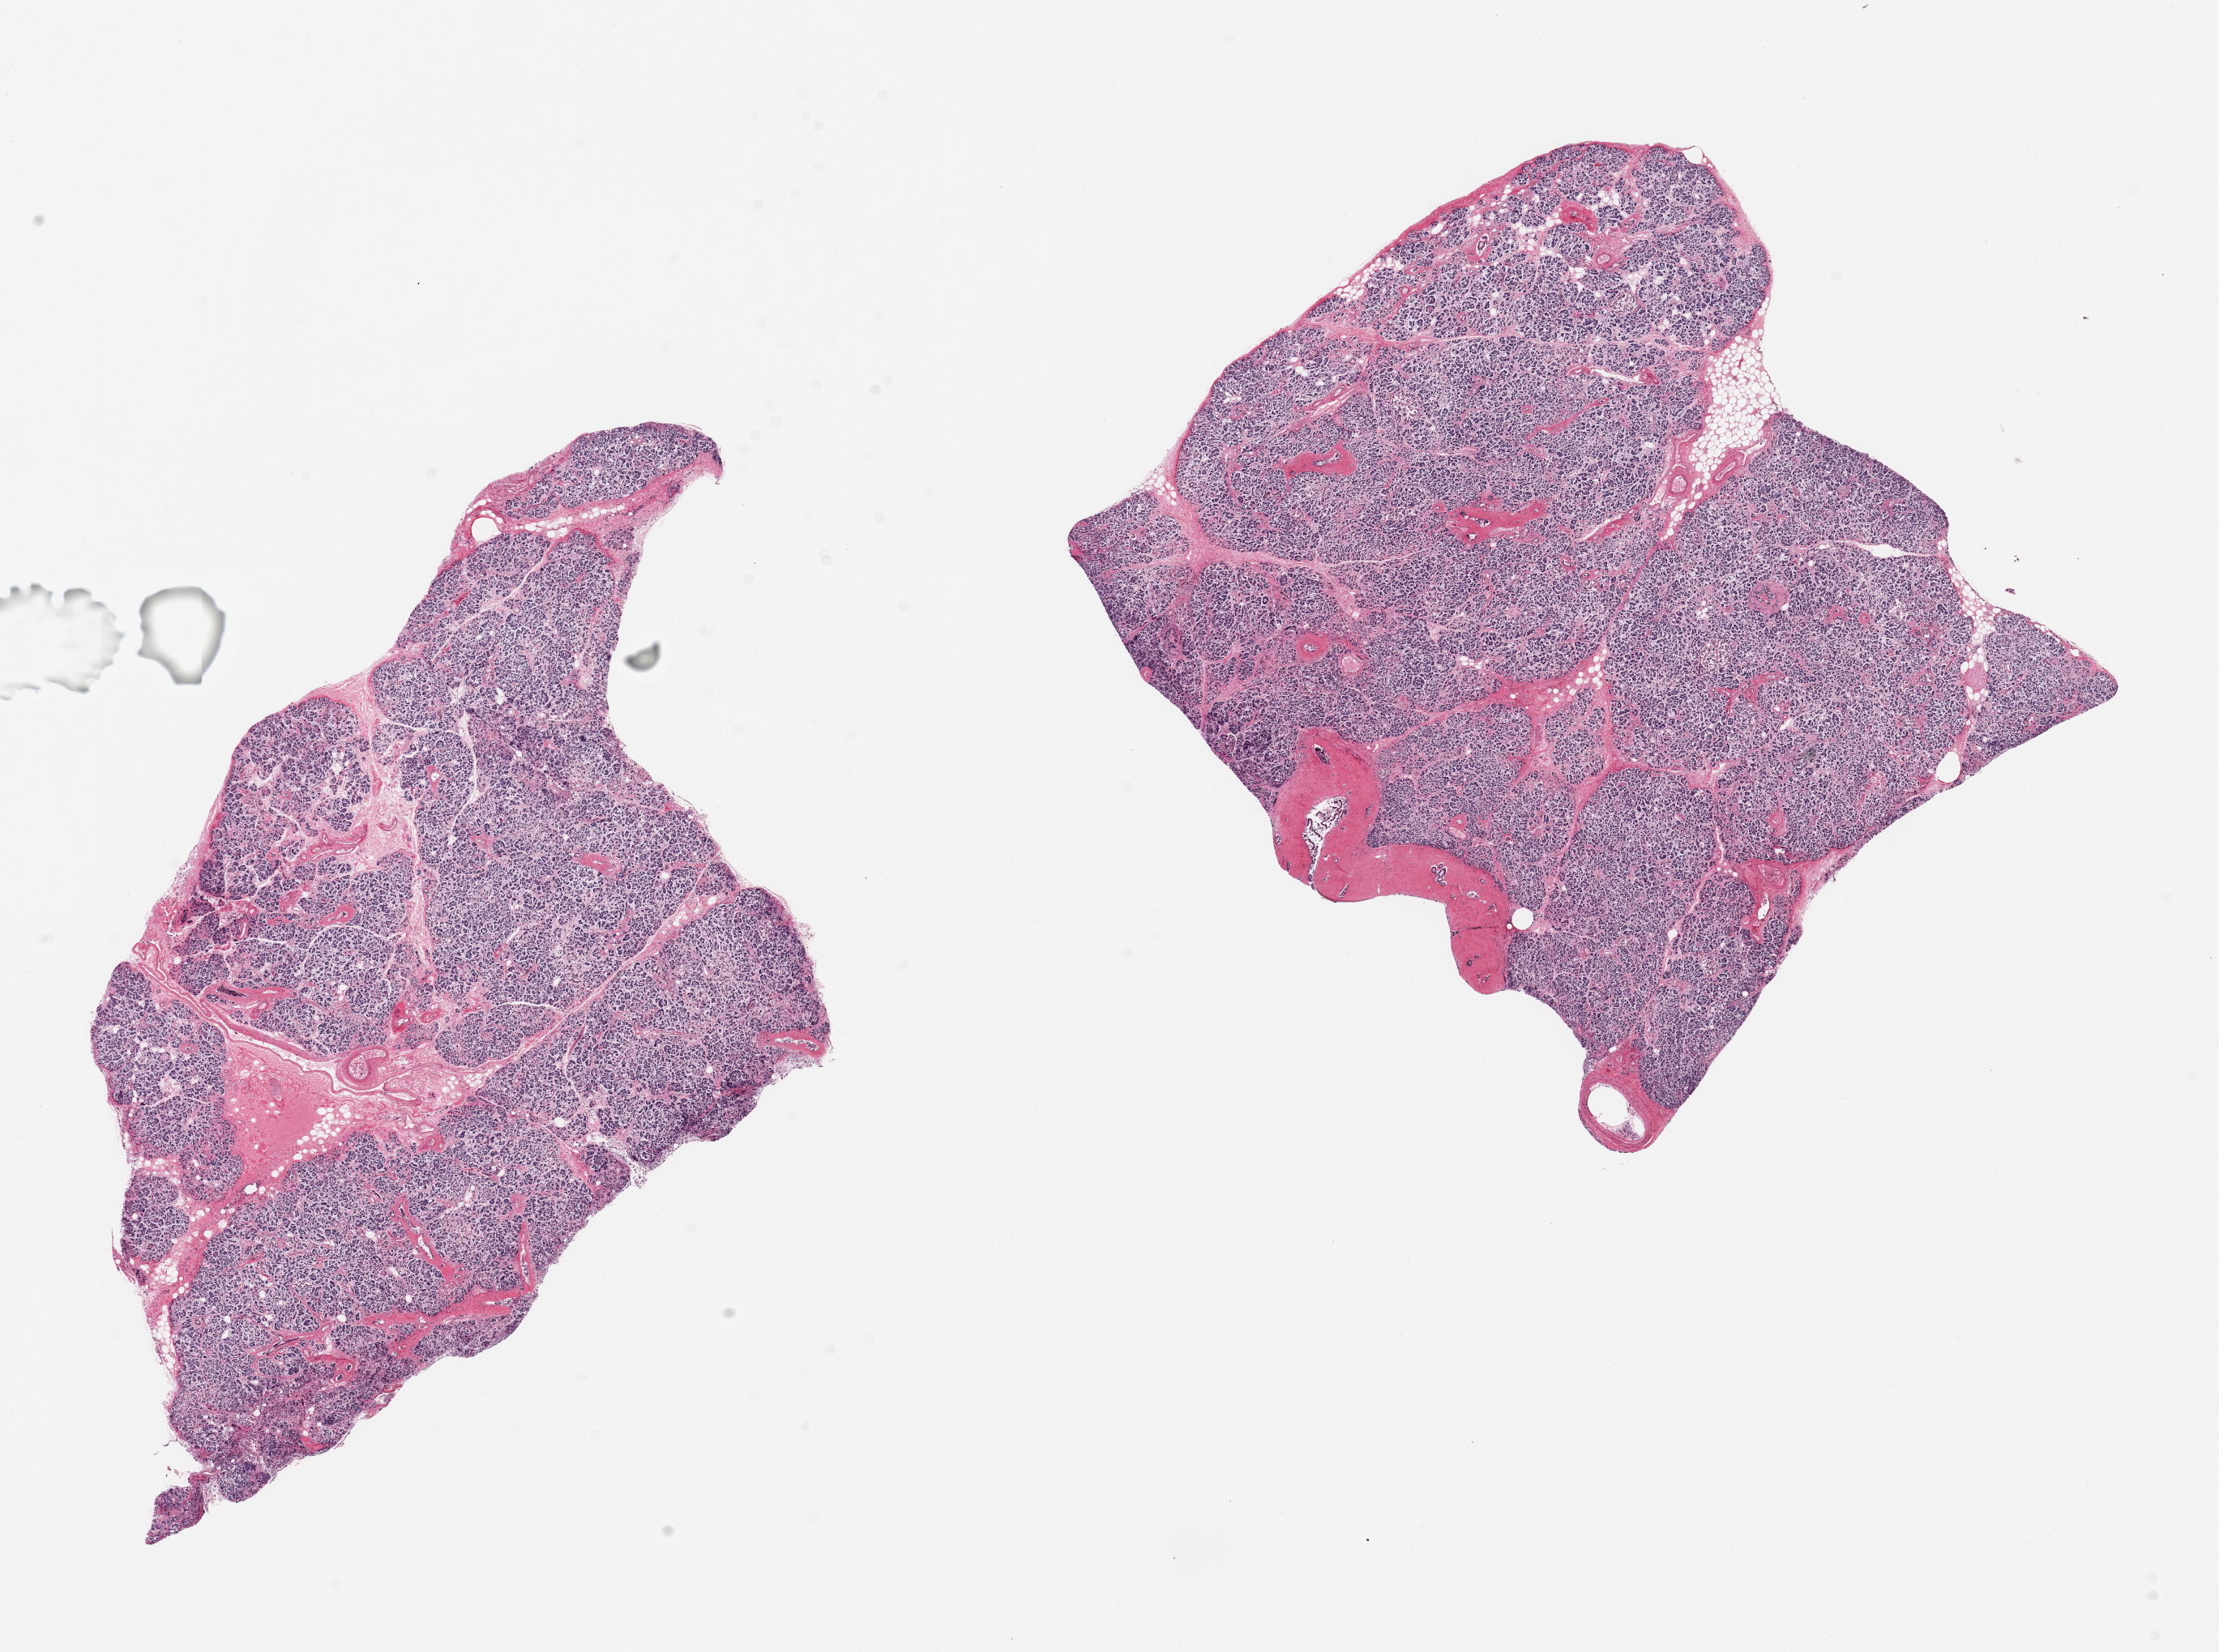
Whole-slide image, hematoxylin and eosin (H&E) stain — low-resolution overview of the scanned area, about 21.7 x 16.1 mm, PAXgene-fixed, paraffin-embedded tissue, target tissue: pancreas, tissue donor sample. Donor: female.
Reviewer comment on this tissue sample: 2 pieces, 10x7 & 9x8mm; <5% internal adipose.